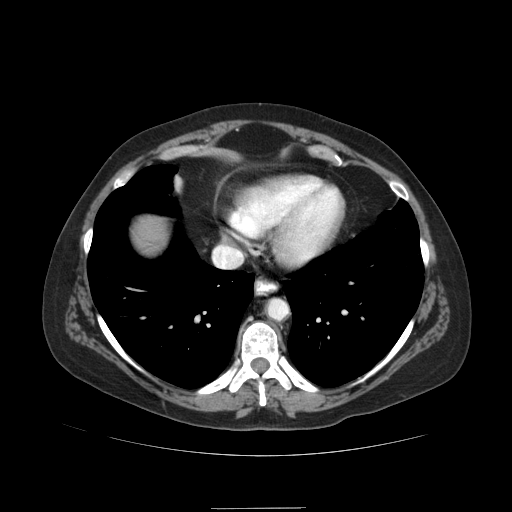
Contrast-enhanced abdominal CT (liver protocol), one axial slice; position 81 of 89 along the scan axis; reconstruction kernel STANDARD; 120 kVp; soft-tissue window (W 400 / L 40 HU); 2.5 mm slice thickness; 512 × 512 image matrix, field of view 400 × 400 mm. From the clinical record (not read from this slice): diagnosis: hepatocellular carcinoma (patient treated with transarterial chemoembolisation; whether this scan precedes or follows treatment is not stated here); TNM stage (as recorded): Stage-IIIB; Child-Pugh class: A; tumour nodularity: multinodular.
Outlined on this slice (semi-automatically segmented with operator editing):
- liver parenchyma outside the tumour (the mass and vessels are separate outlines, so this box may not span the whole liver): bounding box <134,216,166,252> (left, top, right, bottom; pixels)